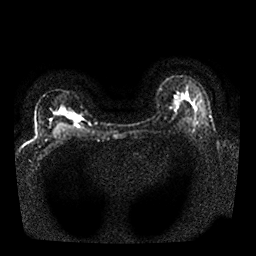
Breast MRI, one axial slice. Position 16 of 25 along the scan axis. Diffusion-weighted series; image 2 of 4 stored at this slice position (different b-values; order by instance number). 1.5 T. 4 mm slice thickness. 256 × 256 image matrix, field of view 340 × 340 mm. Female patient.
Annotated regions visible in this slice (manually delineated by an expert):
- tumour on diffusion-weighted imaging: box from (x=69, y=112) to (x=81, y=123) px